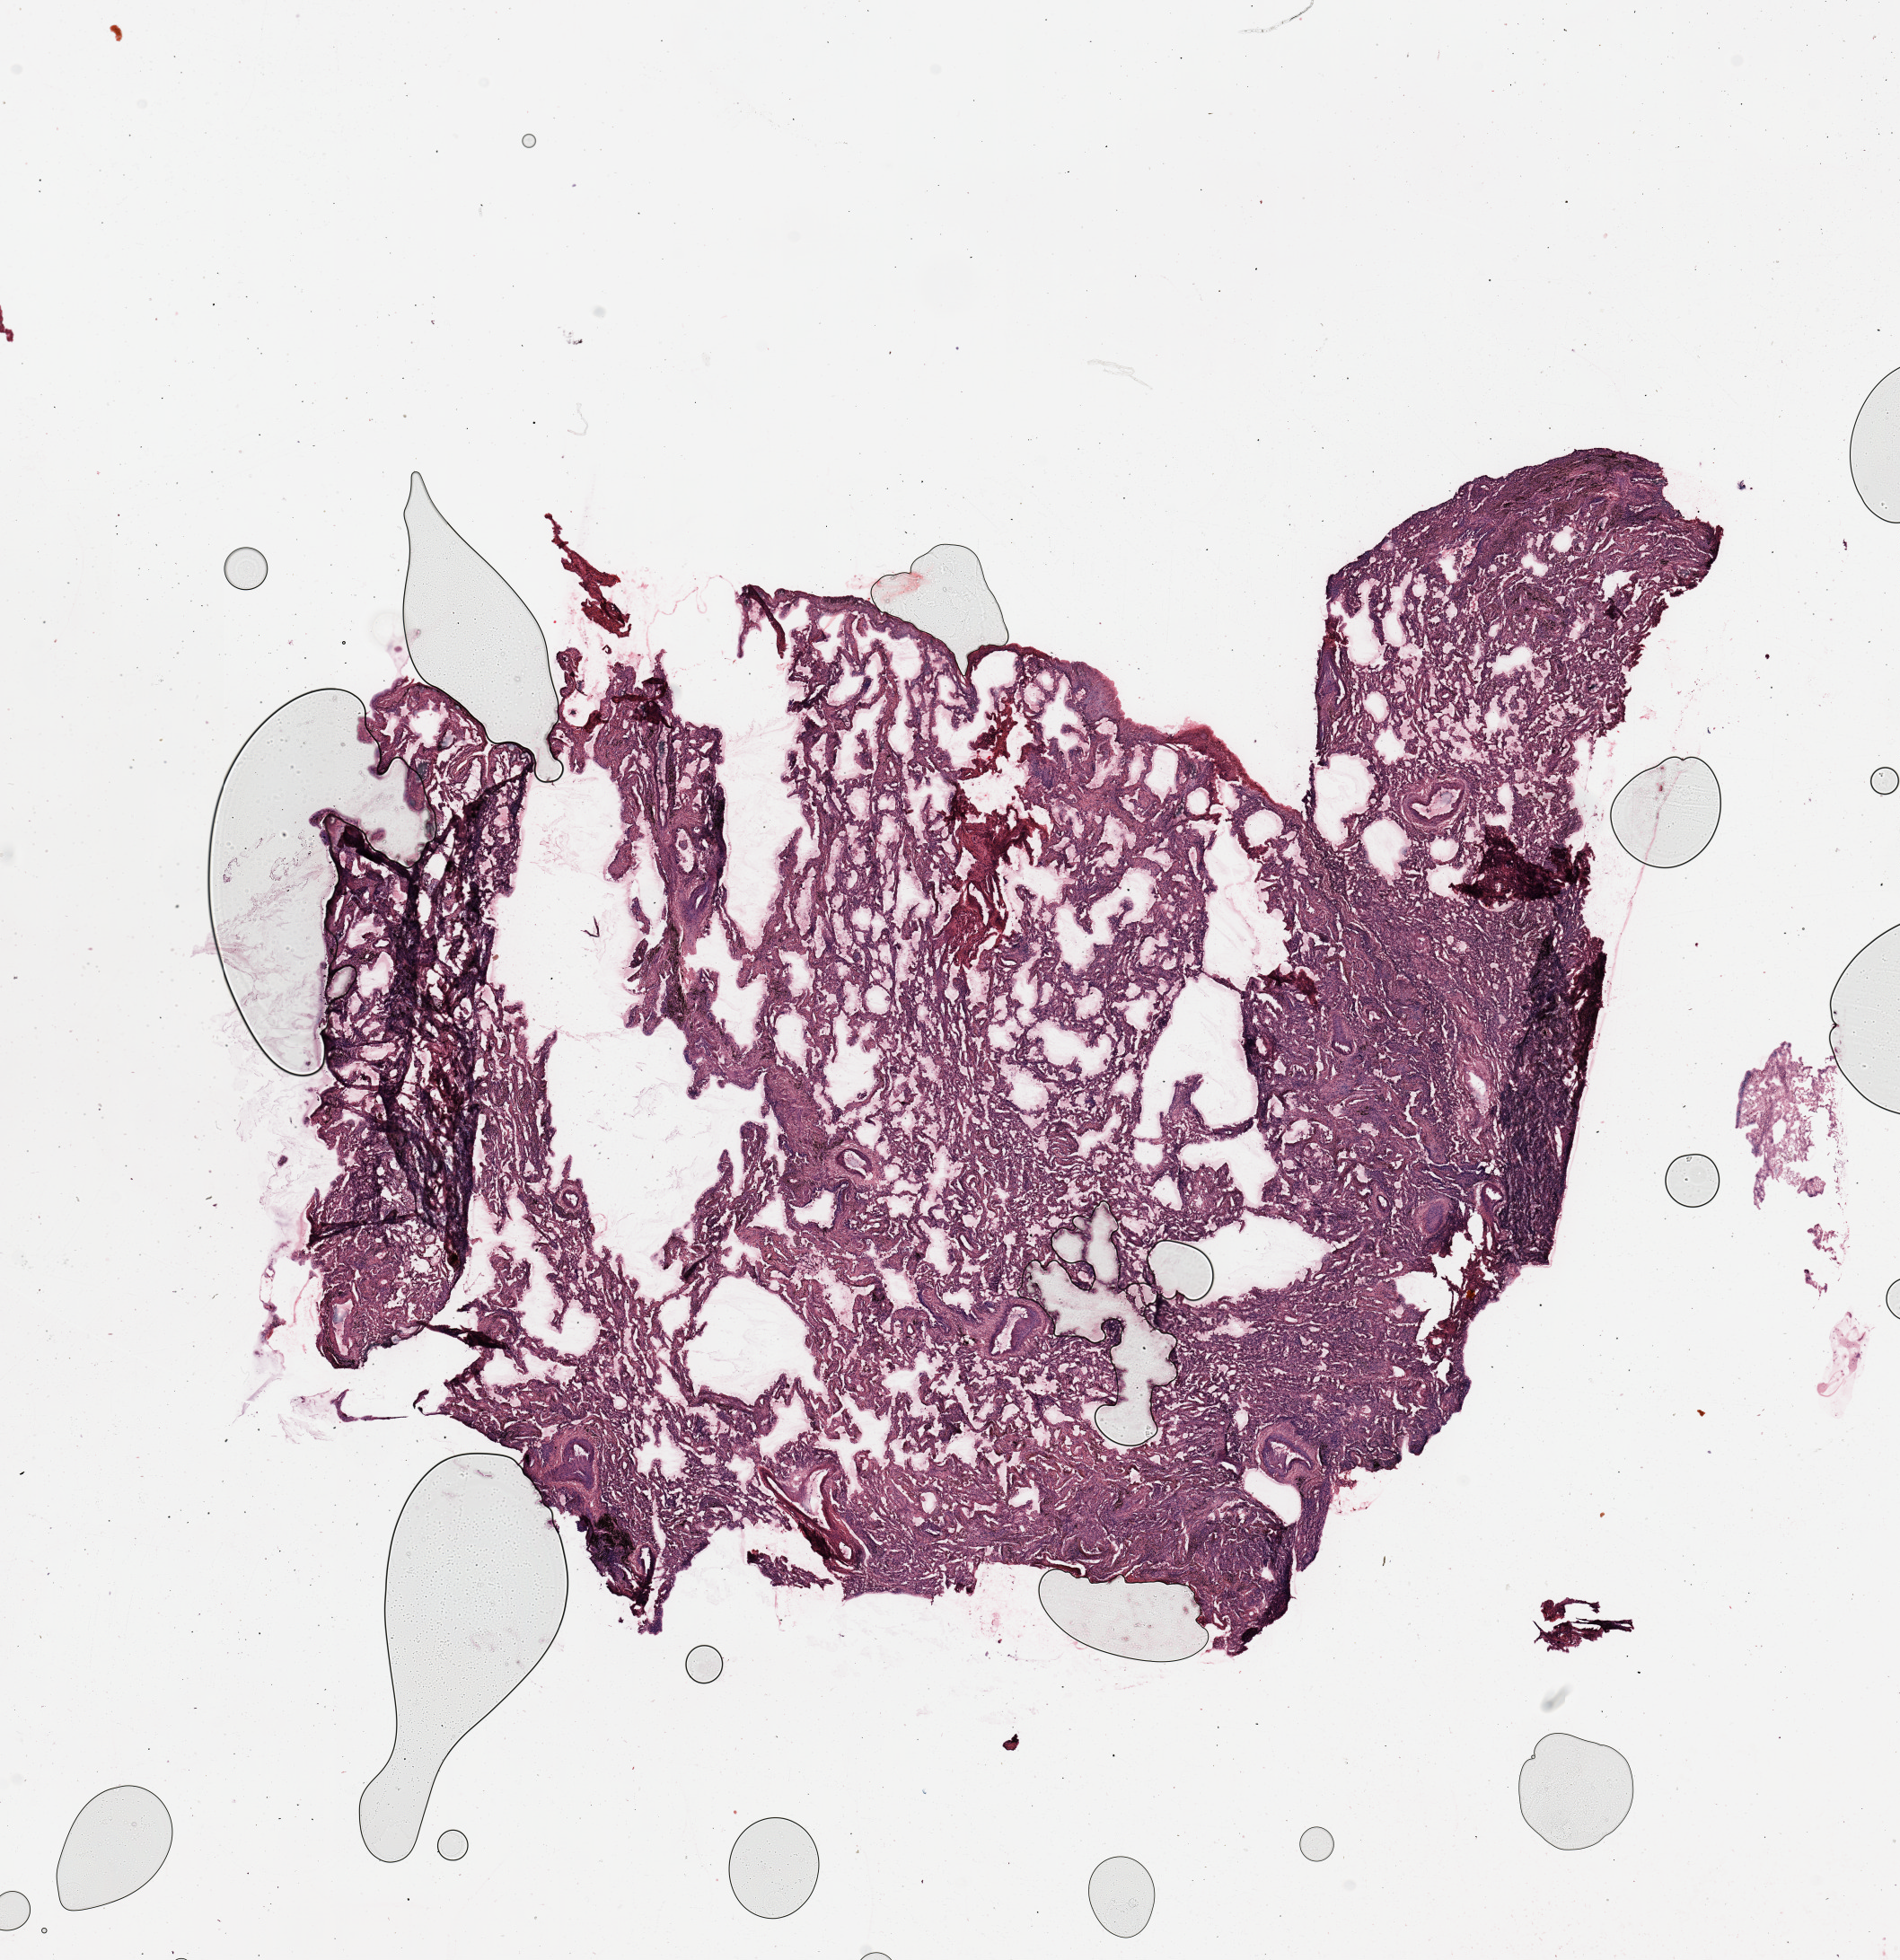
H&E whole-slide image — a low-resolution overview of the entire scanned area, about 16.7 x 17.3 mm (from a 20x scan), normal (non-tumour) tissue sample, lung. 57-year-old male patient.
This section: normal (non-tumour) tissue from the same patient. Patient diagnosis: Adenocarcinoma, NOS.